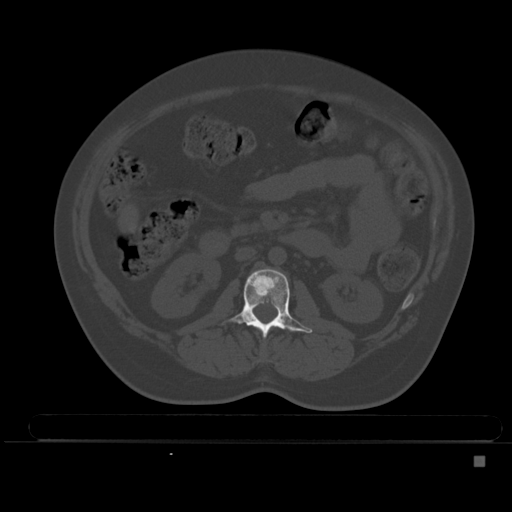
CT including the spine, one axial slice. Slice 174 of 495 in the series (ordered by position). Bone window (W 1800 / L 400 HU). 512 × 512 image matrix, field of view 404 × 404 mm. Female patient, age 33 years. Case-level facts recorded for this patient, not image findings: primary cancer: breast; vertebrae with lytic lesions (as recorded): T1.
Outlined on this slice (semi-automatic segmentation, software-assisted and operator-edited):
- L2 vertebra: box from (x=221, y=269) to (x=312, y=338) px